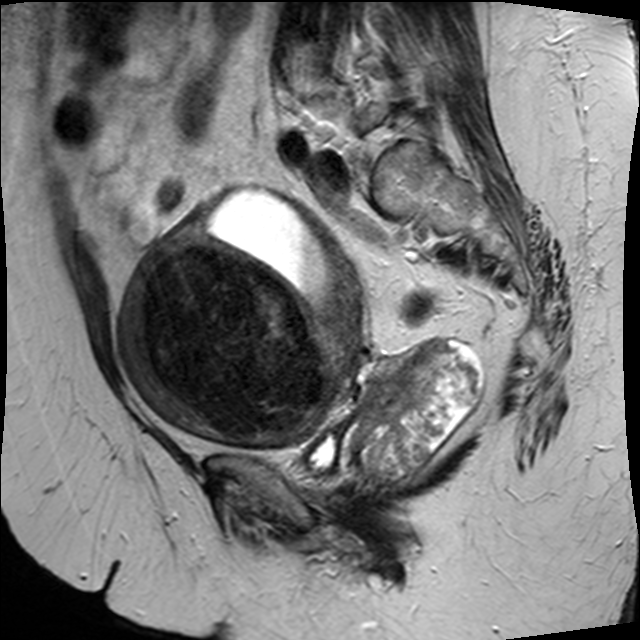
Pelvic MRI for cervical cancer, one sagittal slice. Slice 13 of 34 in the series (ordered by position). T2-weighted. 1.5 T. TE 89 ms, TR 3320 ms. 4 mm slice thickness. 640 × 640 image matrix, field of view 260 × 260 mm. Female patient, age 50 years.
Outlined on this slice (manually delineated by an expert):
- uterus and cervix: bounding box (x1, y1, x2, y2) in pixels: (120, 188, 481, 484)